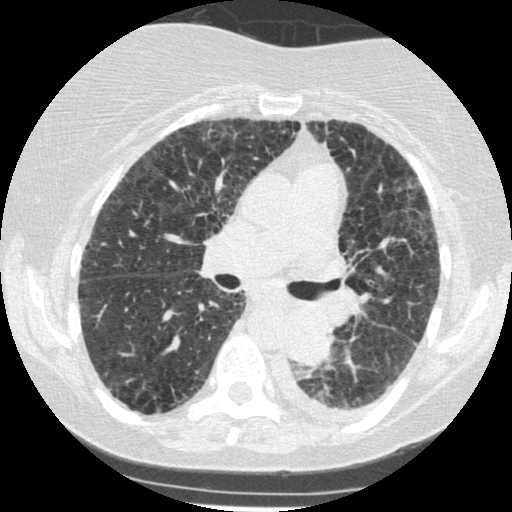
Low-dose screening chest CT, axial slice. Third screening round (two years after baseline). Lung window (W 1500 / L -600 HU). 1.25 mm slice thickness. Slice 193 of 341 in the series. Female, age 60 years at enrolment. Former smoker at enrolment.
Expert-annotated lung lesion, box from (x=270, y=307) to (x=342, y=373) px. The exam's reader record, not a measurement of the box and not confirmed to be the same lesion: non-calcified nodule or mass ≥4 mm, left lower lobe, 54 × 38 mm, smooth margins, soft tissue attenuation, pre-existing on the prior screen: yes; interval growth: yes. Participant outcome: lung cancer diagnosed 15 days after this screen — small cell carcinoma, NOS, left lower lobe, undifferentiated (G4), stage IV (AJCC 6th edition), 69 mm at pathology.